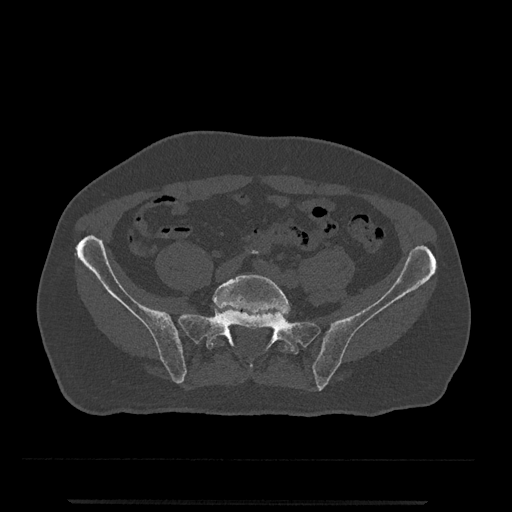
CT including the spine, one axial slice; slice 38 of 797 in the series (ordered by position); reconstruction kernel Br40s/3; 120 kVp; bone window (W 1800 / L 400 HU); 512 × 512 image matrix, field of view 419 × 419 mm. Patient: male, 63 years. From the clinical record (not read from this slice): primary cancer: prostate.
Structures marked on this image (semi-automatically segmented with operator editing):
- L5 vertebra: bounding box [x1, y1, x2, y2] px = [209, 274, 290, 352]